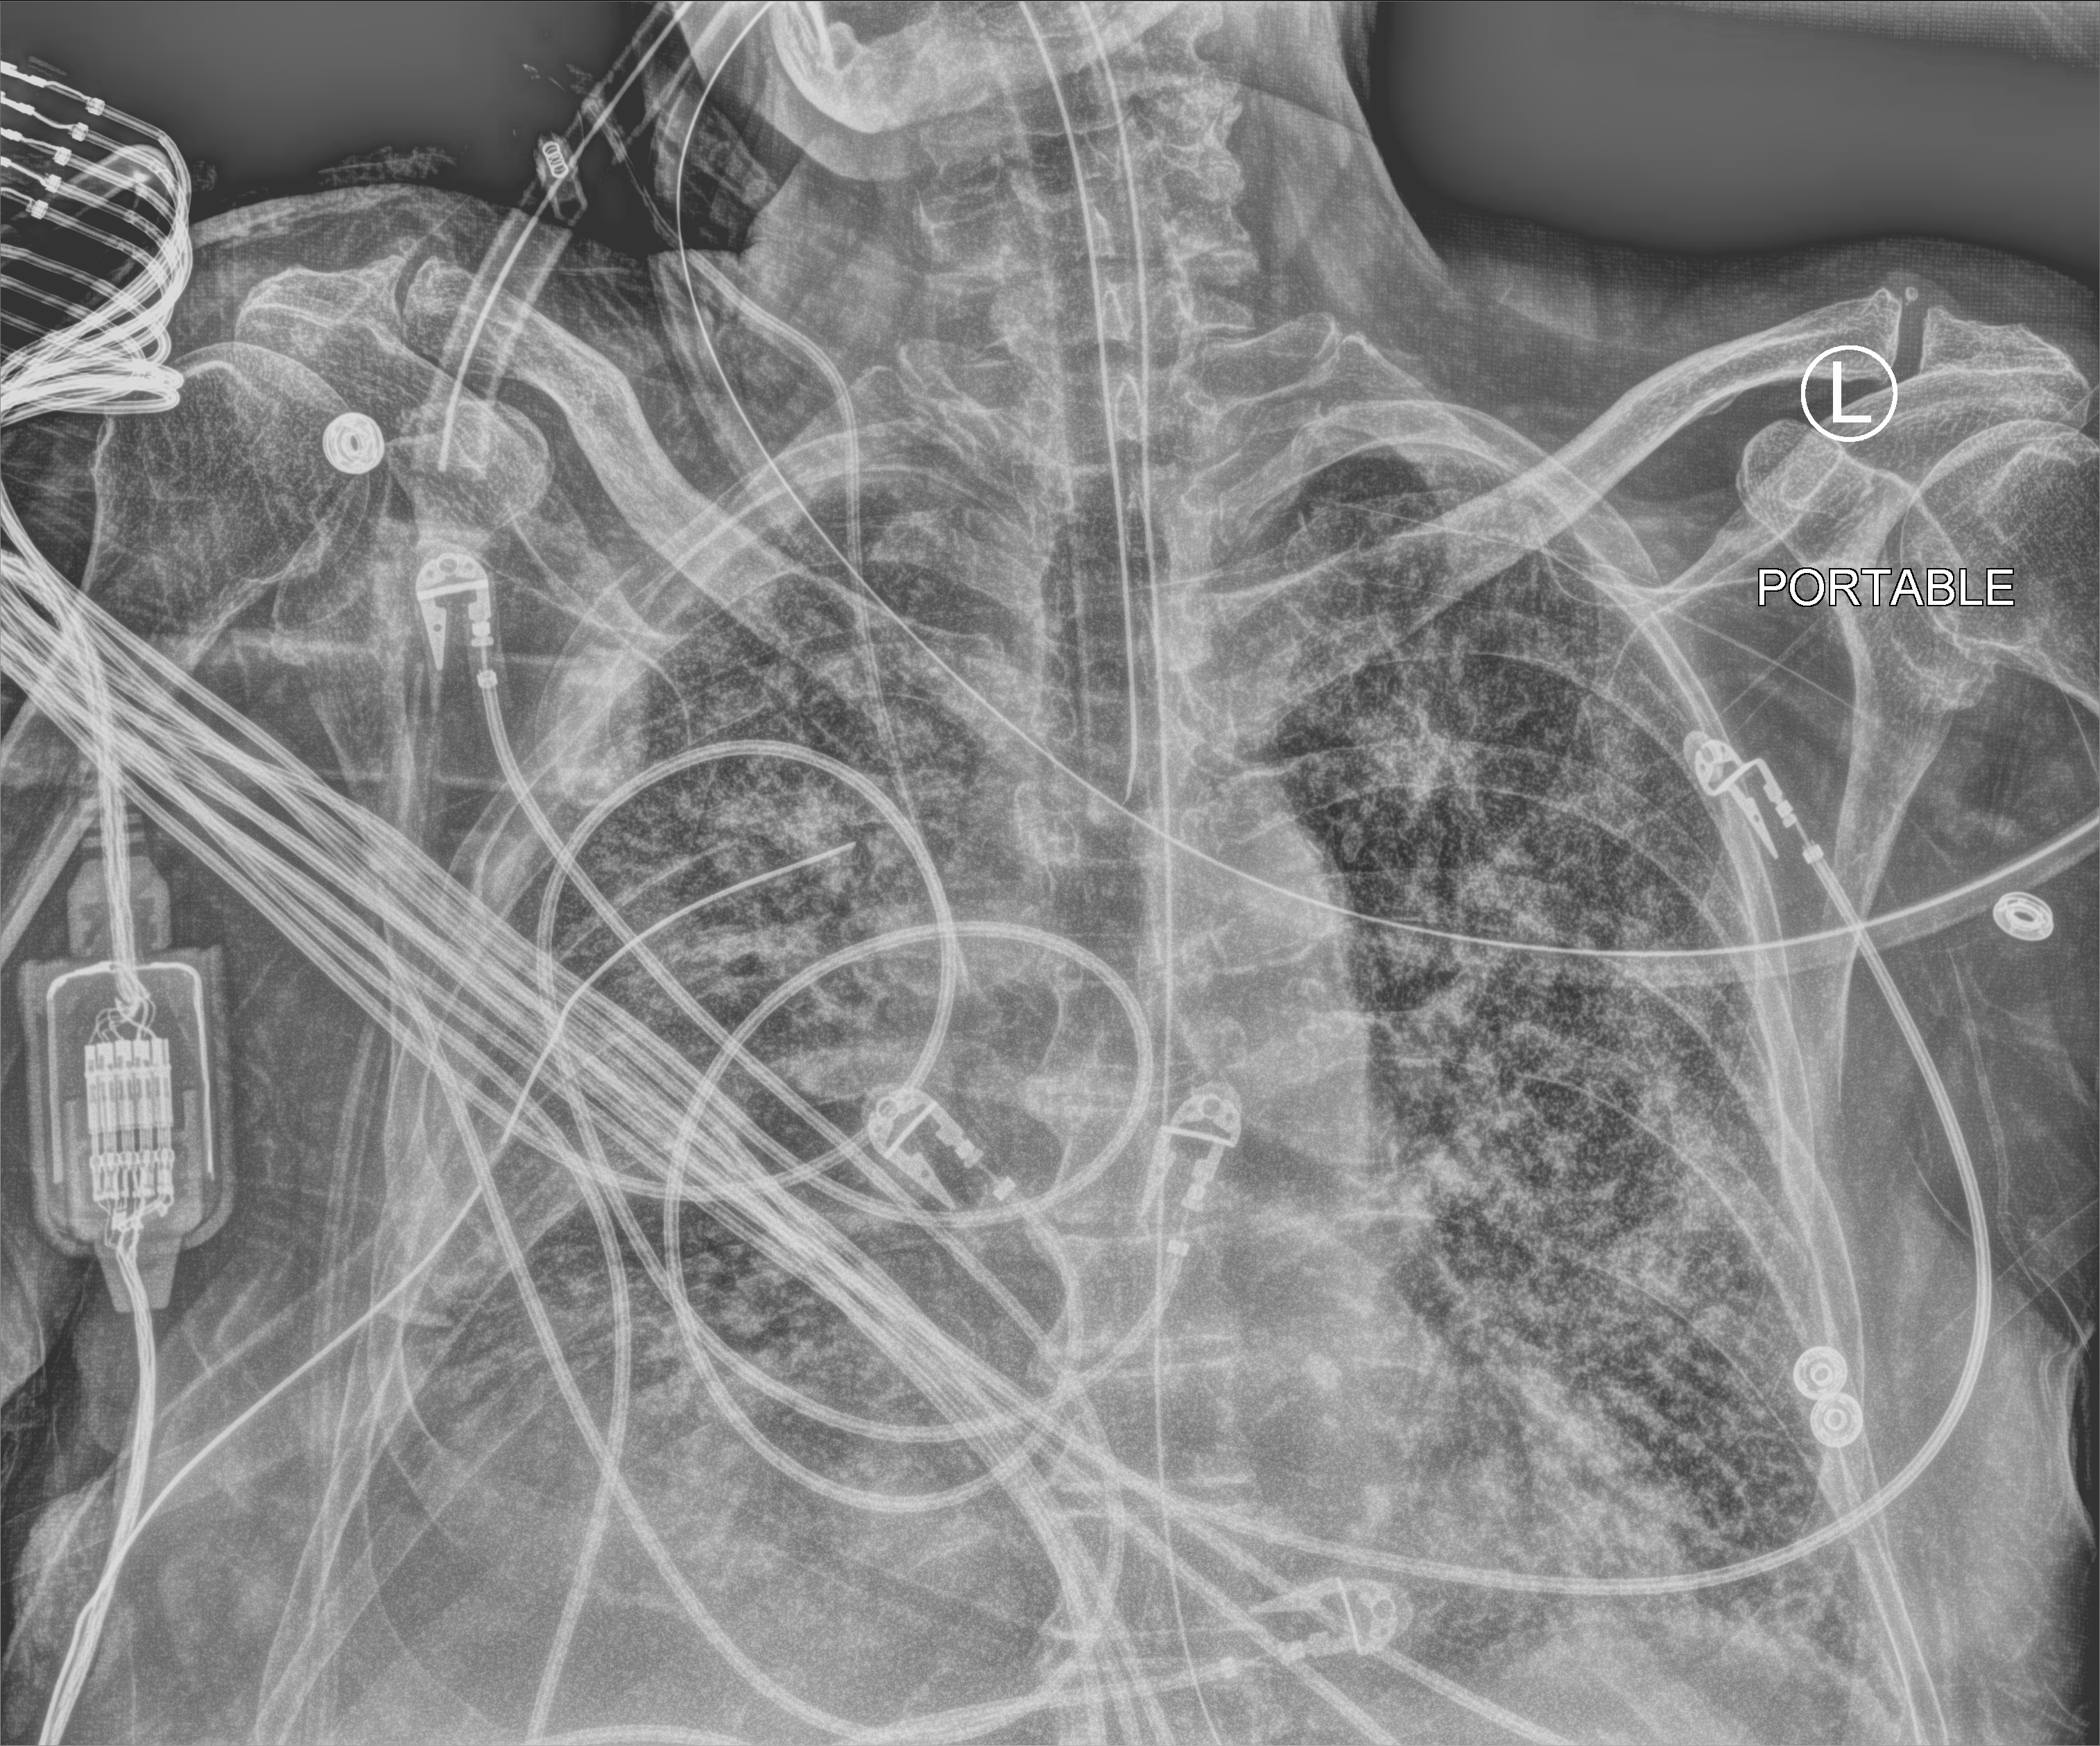
Chest X-ray (portable); anteroposterior (AP) projection. Patient hospitalised with COVID-19; male, aged 75–90 years.
Hospital-stay facts (about this admission, not read from this image; timing relative to this image not recorded): COPD (admission record): no; mechanically ventilated during this hospital stay: yes.